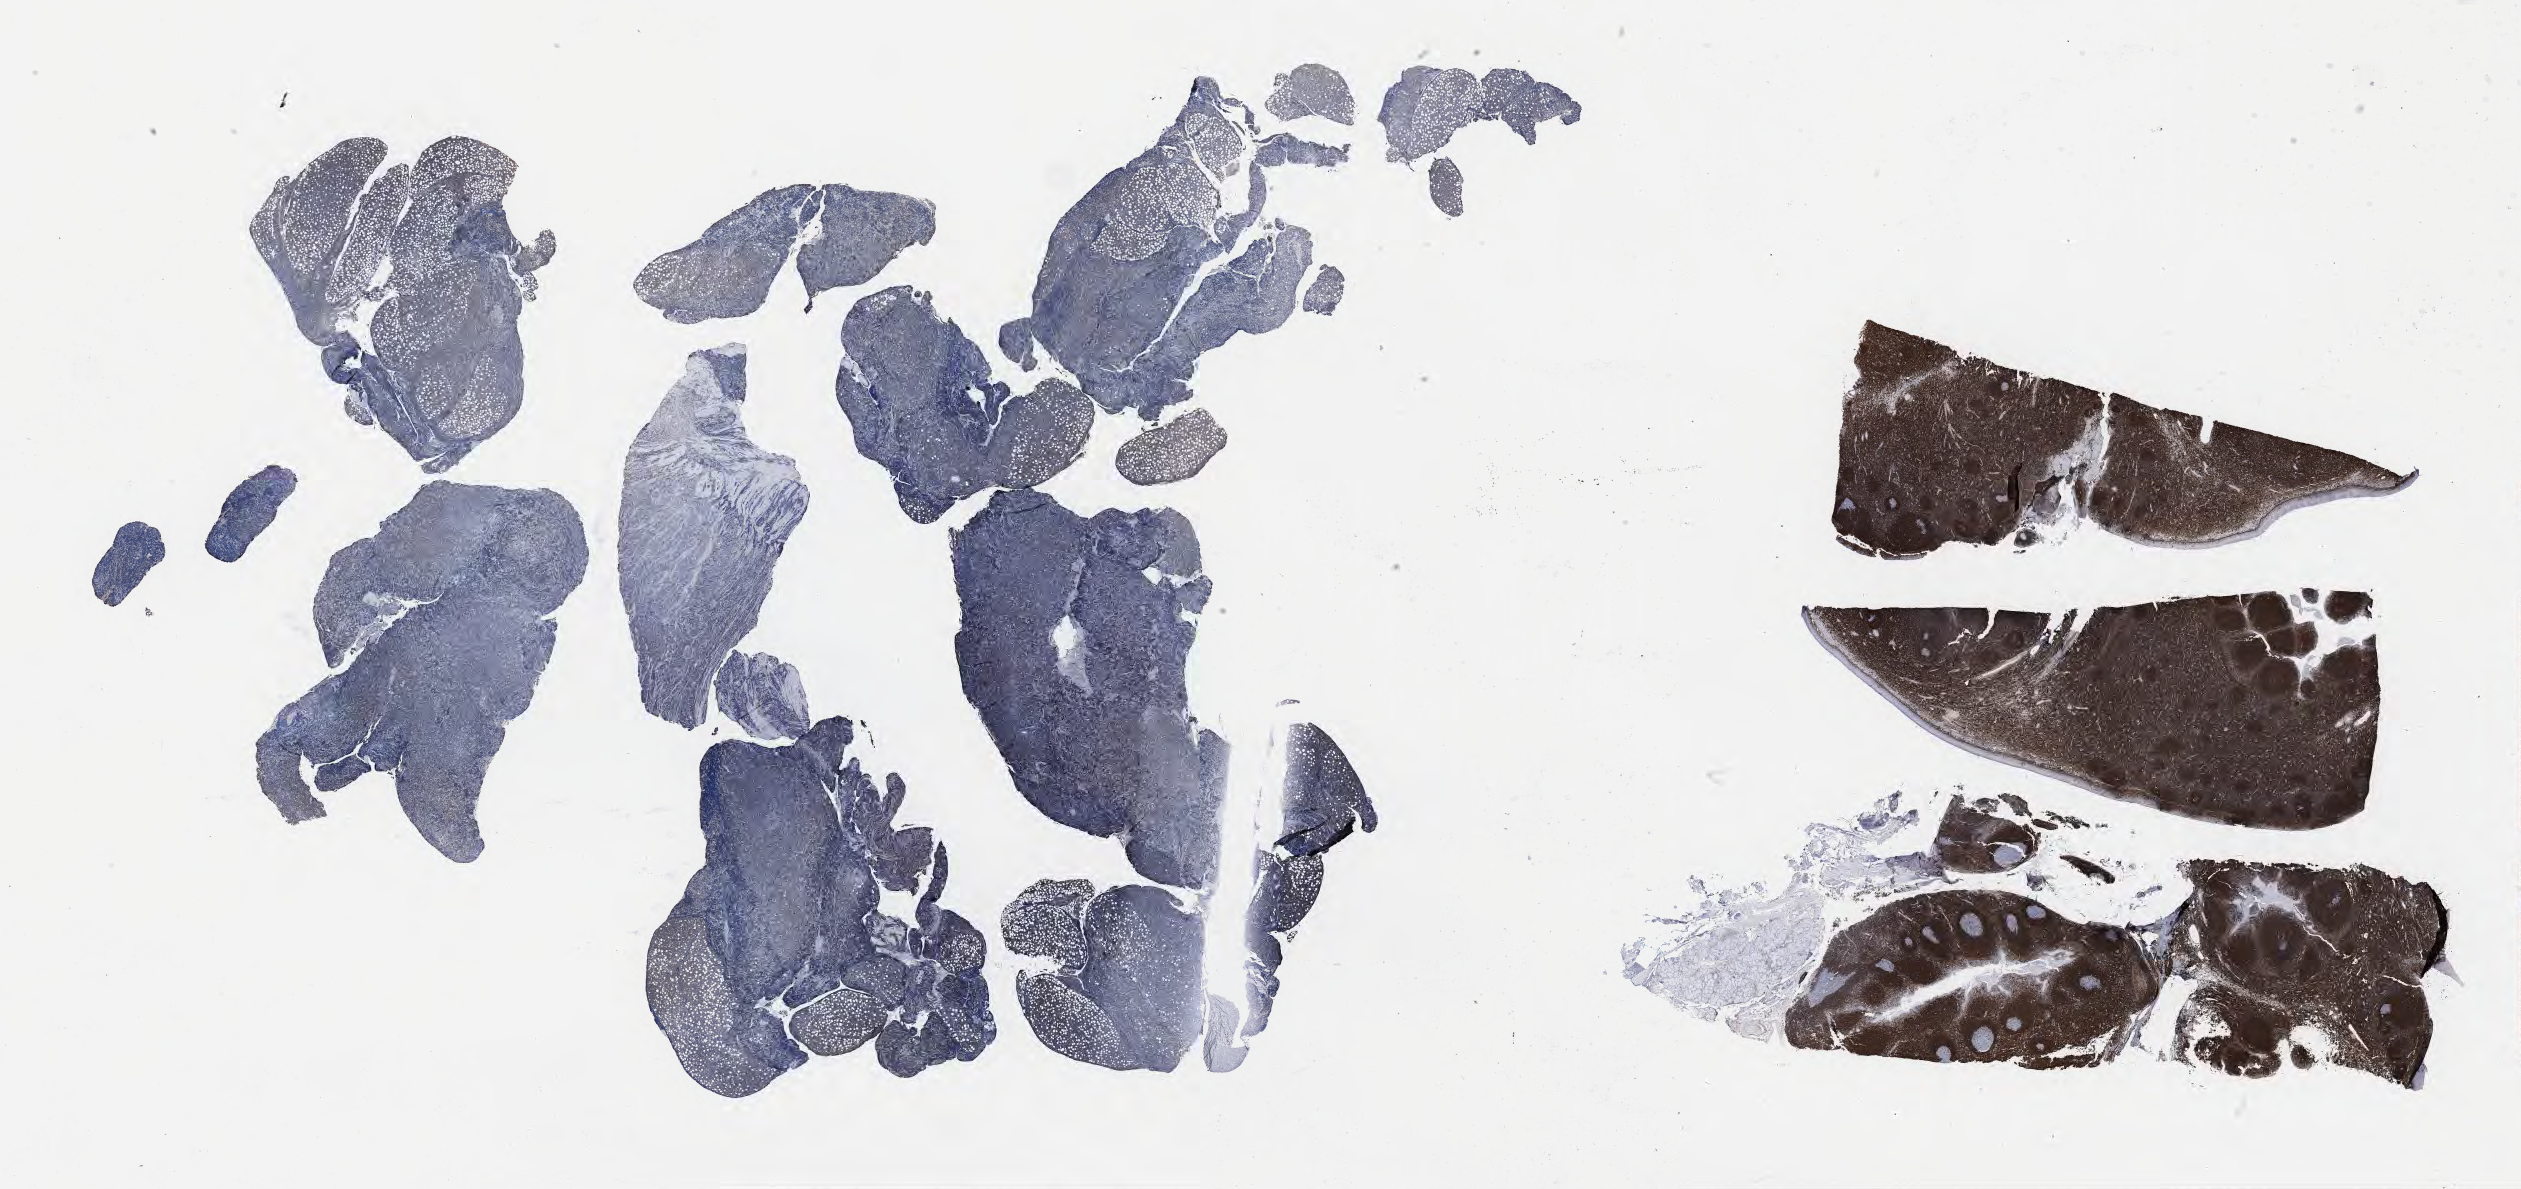
Immunohistochemistry (IHC) whole-slide image stained for BCL2 — whole scanned area (about 40.8 x 19.2 mm) shown as a low-resolution overview, tumor tissue, anatomic site: abdomen proper. Male patient; age at initial diagnosis 4 years.
Diagnosis: Burkitt lymphoma, NOS.